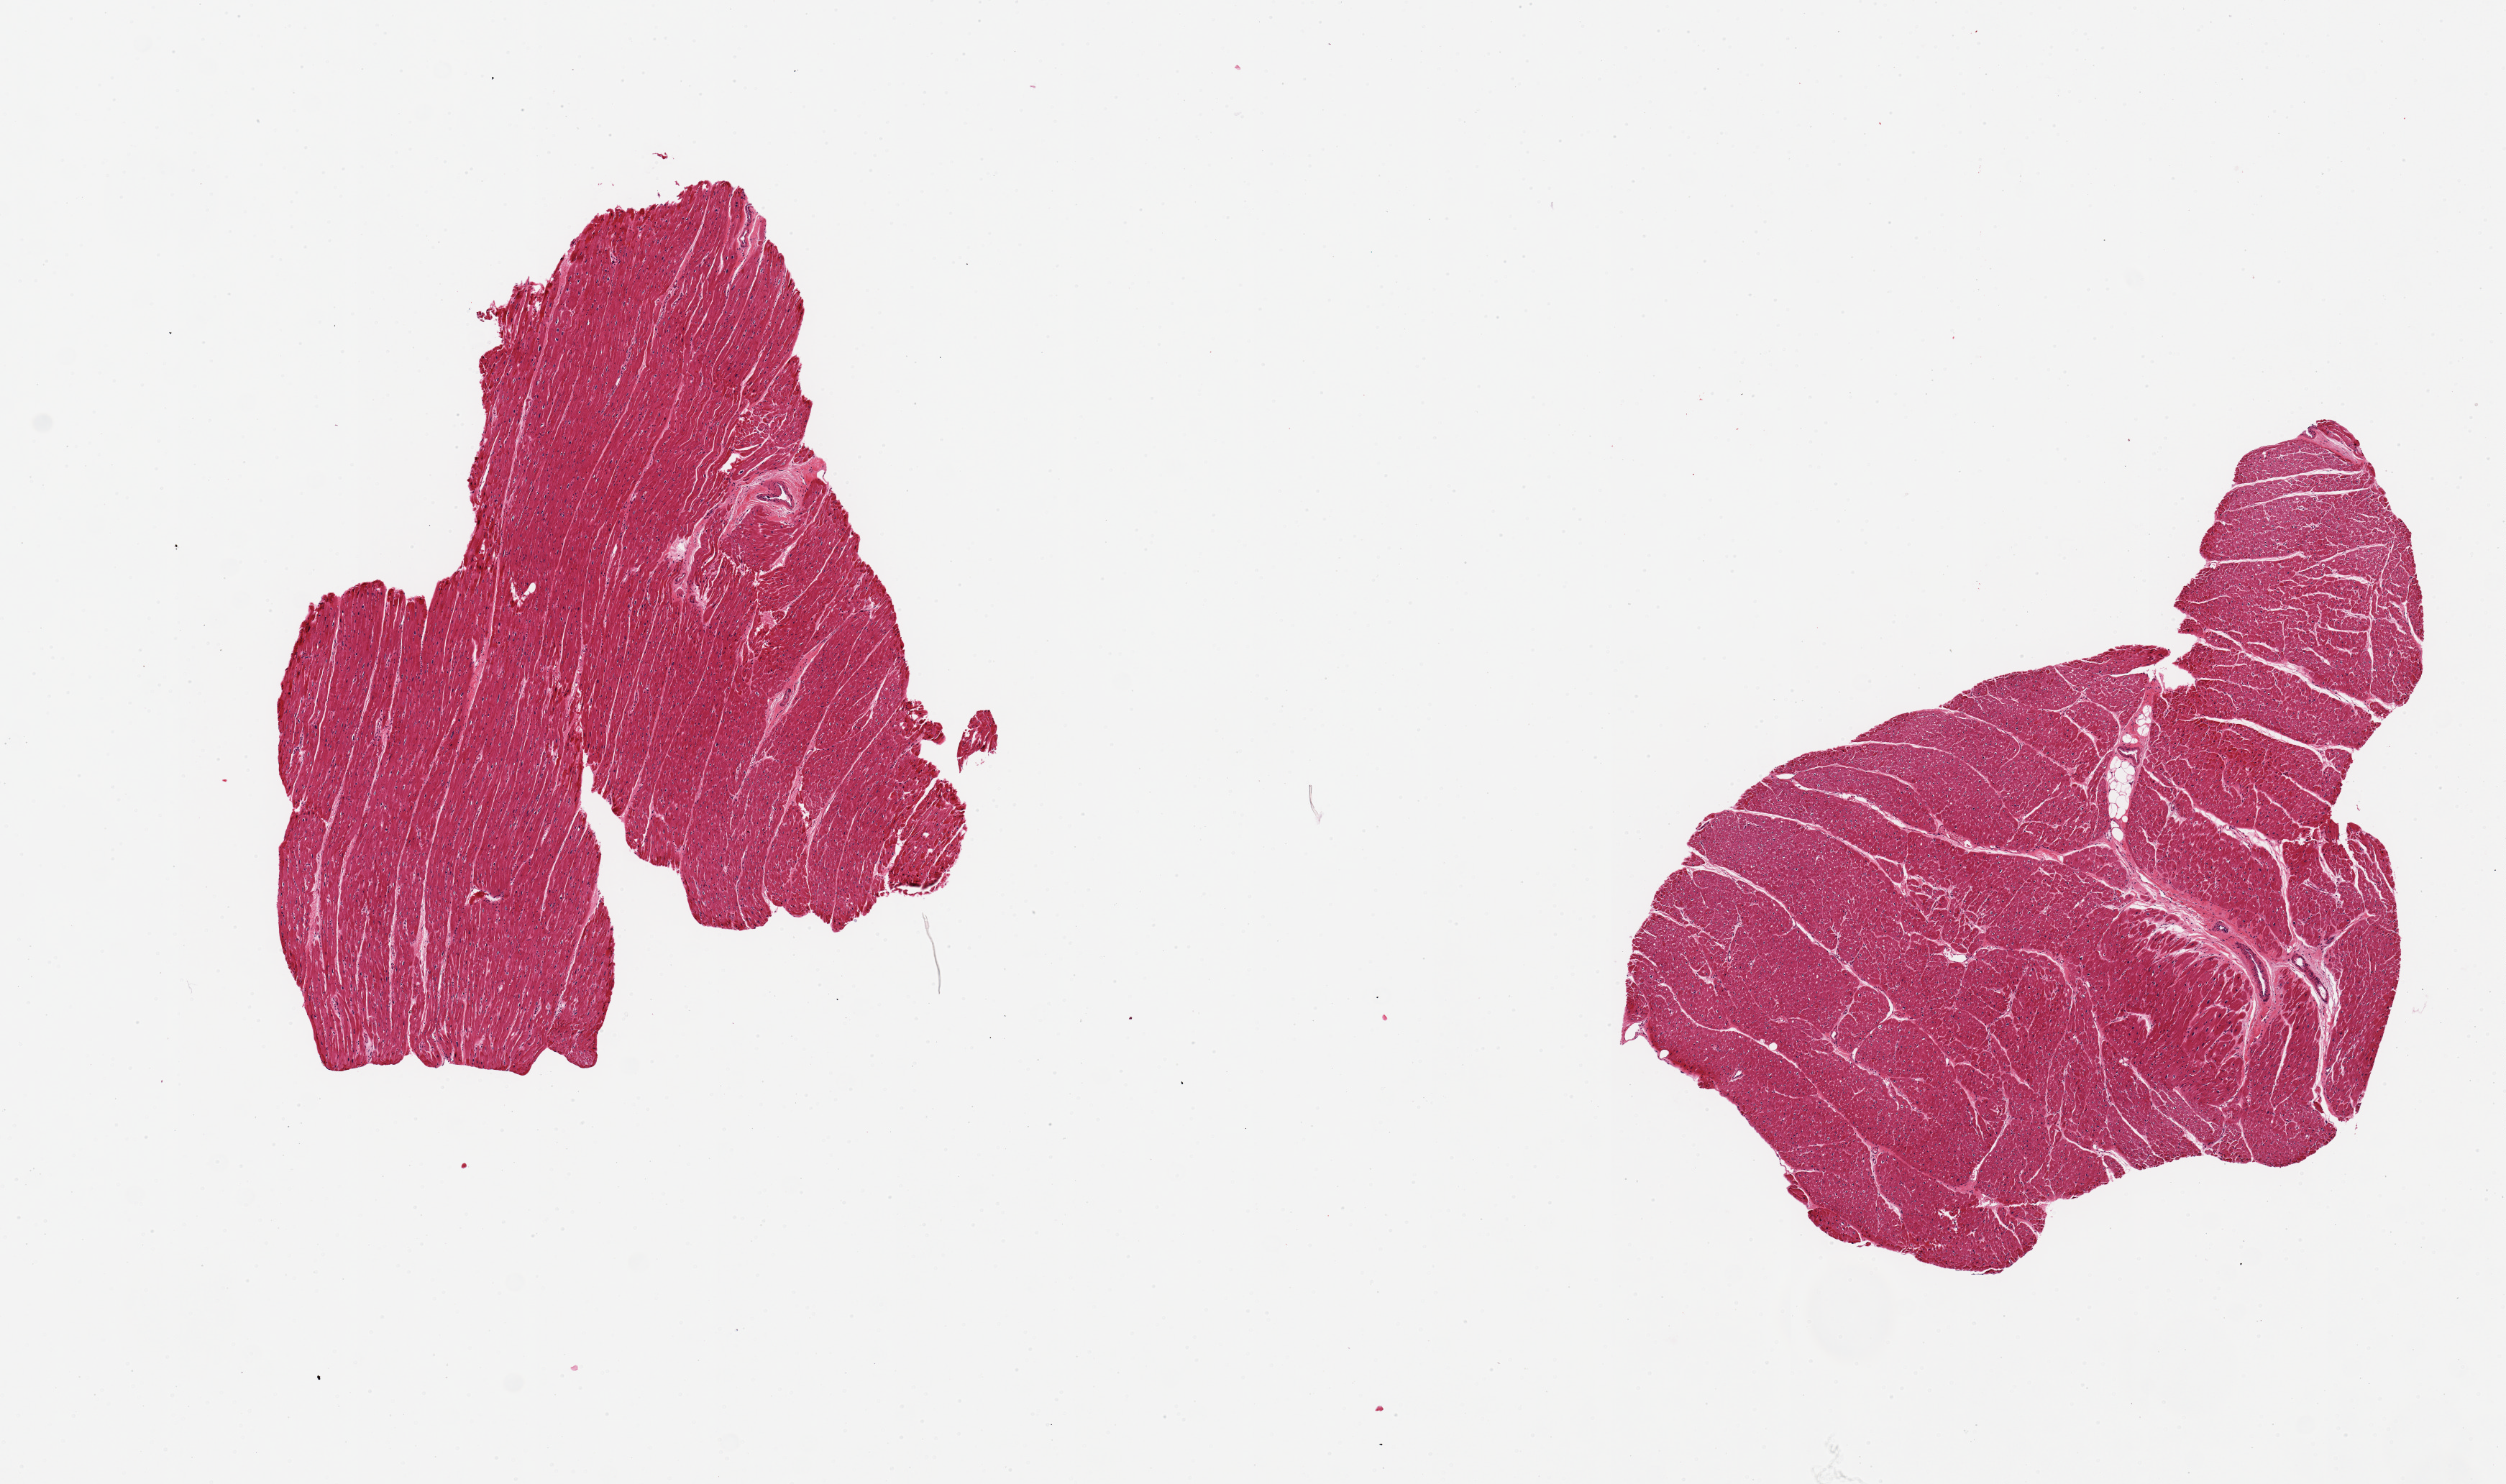
Whole-slide image, H&E stain — shown as a low-resolution overview of the whole scanned area (about 13.8 x 8.2 mm); PAXgene-fixed paraffin-embedded (PFPE) section; target tissue: heart; tissue donor sample. Donor: female.
• pathologist's review note for this sample: 2 pieces, heart specimen